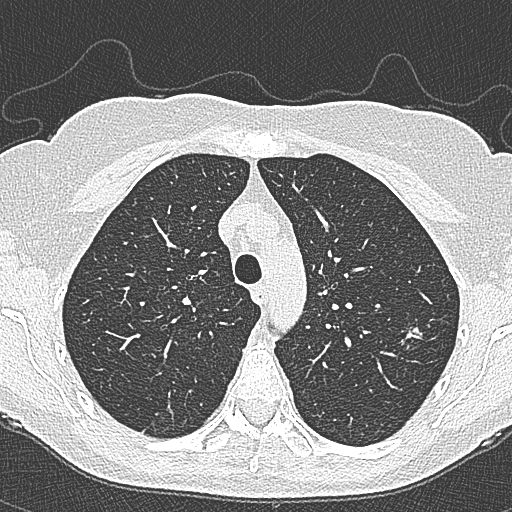
Chest CT (low-dose screening protocol), one axial image. Second screening round (one year after baseline). Lung window (W 1500 / L -600 HU). Lung (sharp) reconstruction kernel (B80f). 512 × 512 image matrix. Female participant, aged 65 years at enrolment. Current smoker at enrolment.
- Lesion marked by an expert reader, box from (x=396, y=311) to (x=444, y=360) px.
- The screening reader recorded 4 non-calcified nodules or masses ≥4 mm on this exam (left upper lobe, left upper lobe, left upper lobe, right lower lobe); which of them this box marks is not recorded.
- Official screen result: positive, change unspecified: nodule(s) >= 4 mm or enlarging nodule(s), mass(es), or other non-specific abnormalities suspicious for lung cancer.
- Lung cancer was diagnosed 54 days after this screen: bronchiolo-alveolar carcinoma, non-mucinous, left upper lobe, stage IA (AJCC 6th edition), 10 mm at pathology.